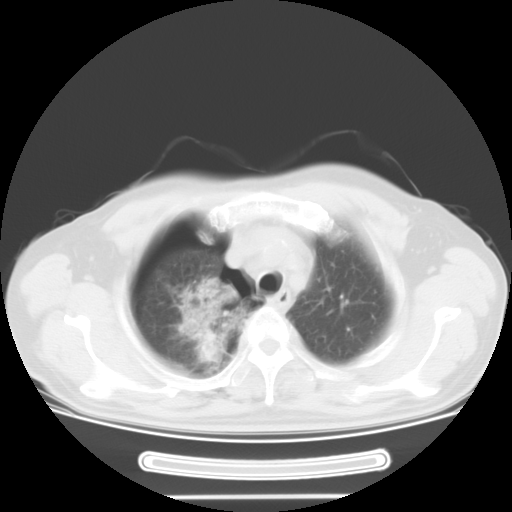
Chest CT, one axial slice. Slice 24 of 29 in the series (ordered by position). Reconstruction kernel STANDARD. Lung window (W 1500 / L -600 HU). 10 mm slice thickness. 512 × 512 image matrix. Male patient, age 61 years. From the clinical record (not read from this slice): clinical TNM (as recorded): T1c N3 M1b.
Outlined on this slice (rectangle marked by the reading radiologist):
- lung tumour (recorded histology: adenocarcinoma): bounding box [x1, y1, x2, y2] px = [160, 278, 249, 376]